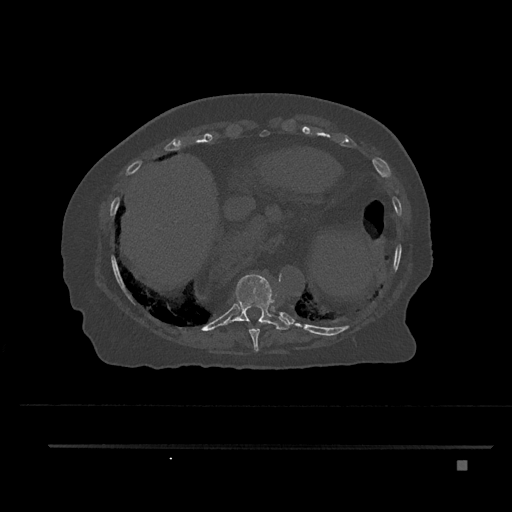
CT including the spine, one axial slice. Slice 371 of 797 in the series (ordered by position). Reconstruction kernel Br40s/3. Bone window (W 1800 / L 400 HU). 0.5 mm slice thickness. 512 × 512 image matrix, field of view 437 × 437 mm. Patient: female, 76 years. Case-level facts recorded for this patient, not image findings: primary cancer: lung; vertebrae with lytic lesions (as recorded): T11, L3.
Annotated regions visible in this slice (semi-automatic segmentation, software-assisted and operator-edited):
- T10 vertebra: bounding box [x1, y1, x2, y2] px = [220, 274, 290, 330]
- T9 vertebra: [248, 320, 265, 351]